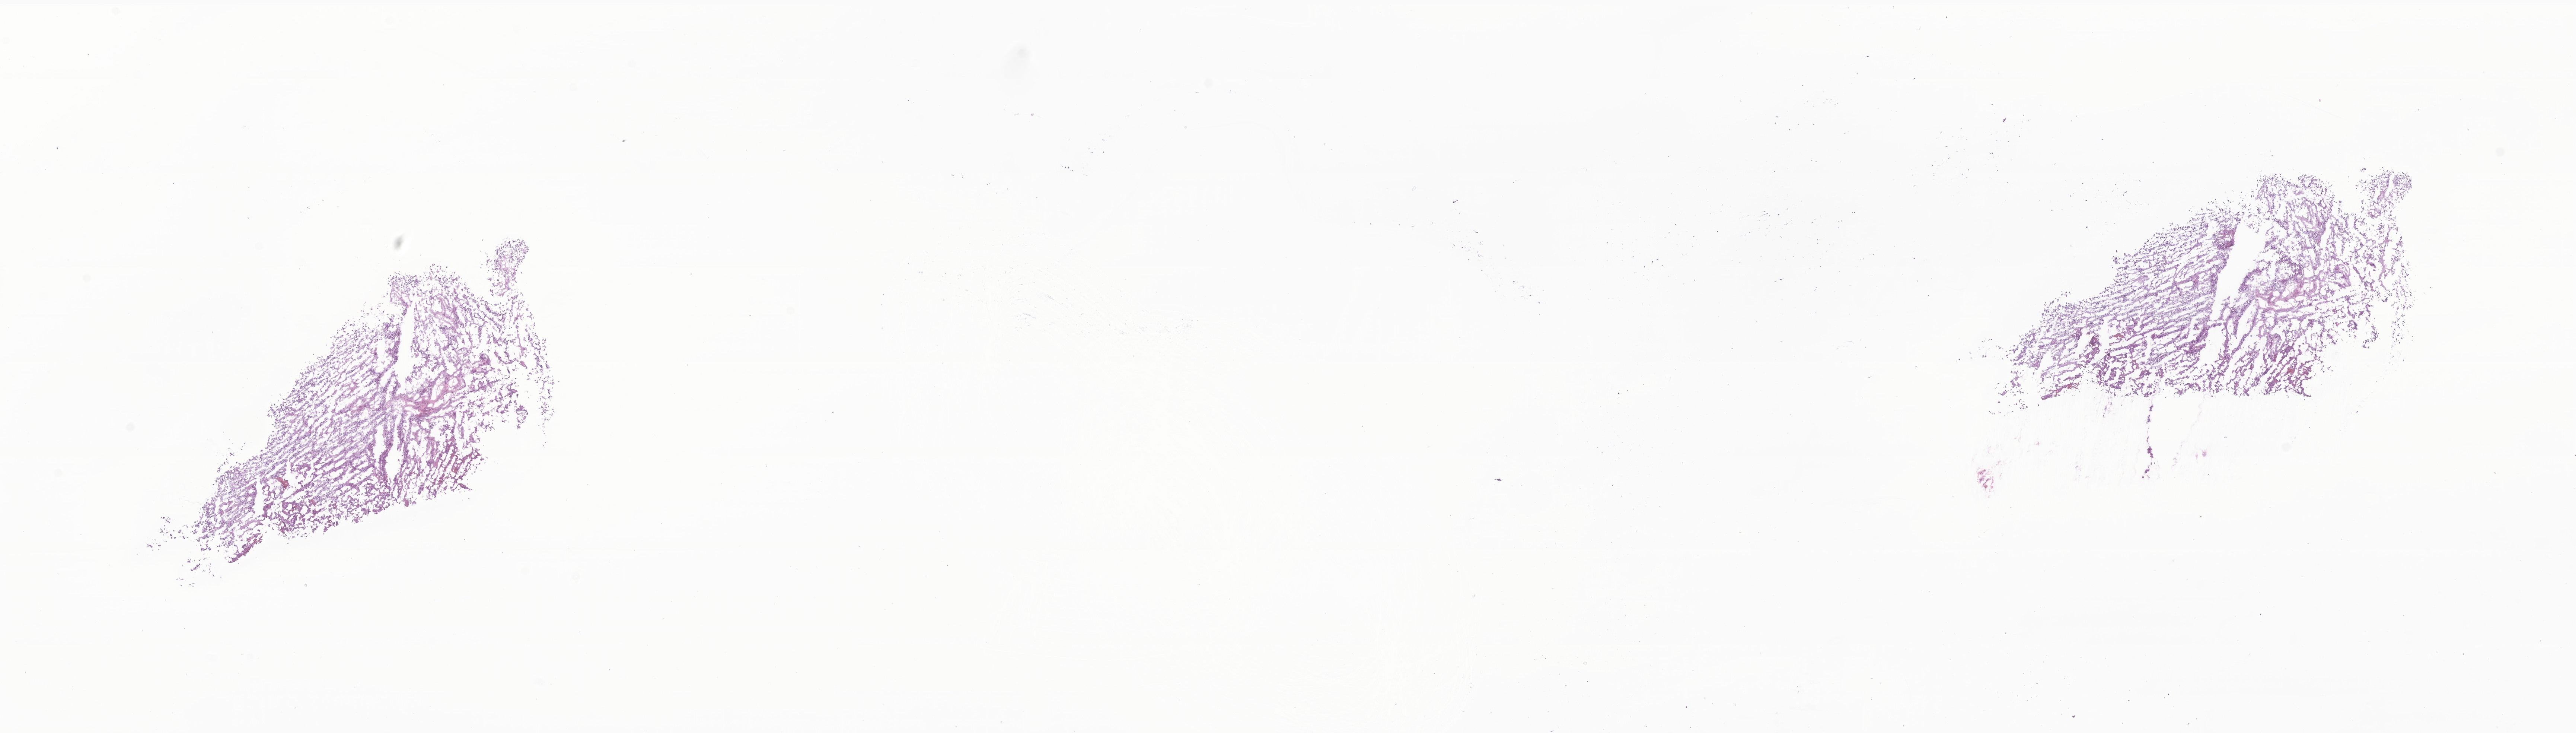
Hematoxylin and eosin (H&E) whole-slide image of tumor tissue from the brain, low-resolution overview of the scanned area, about 29.2 x 8.3 mm. Frozen section. Female patient, age 104 months.
* recorded diagnosis: Astroblastoma